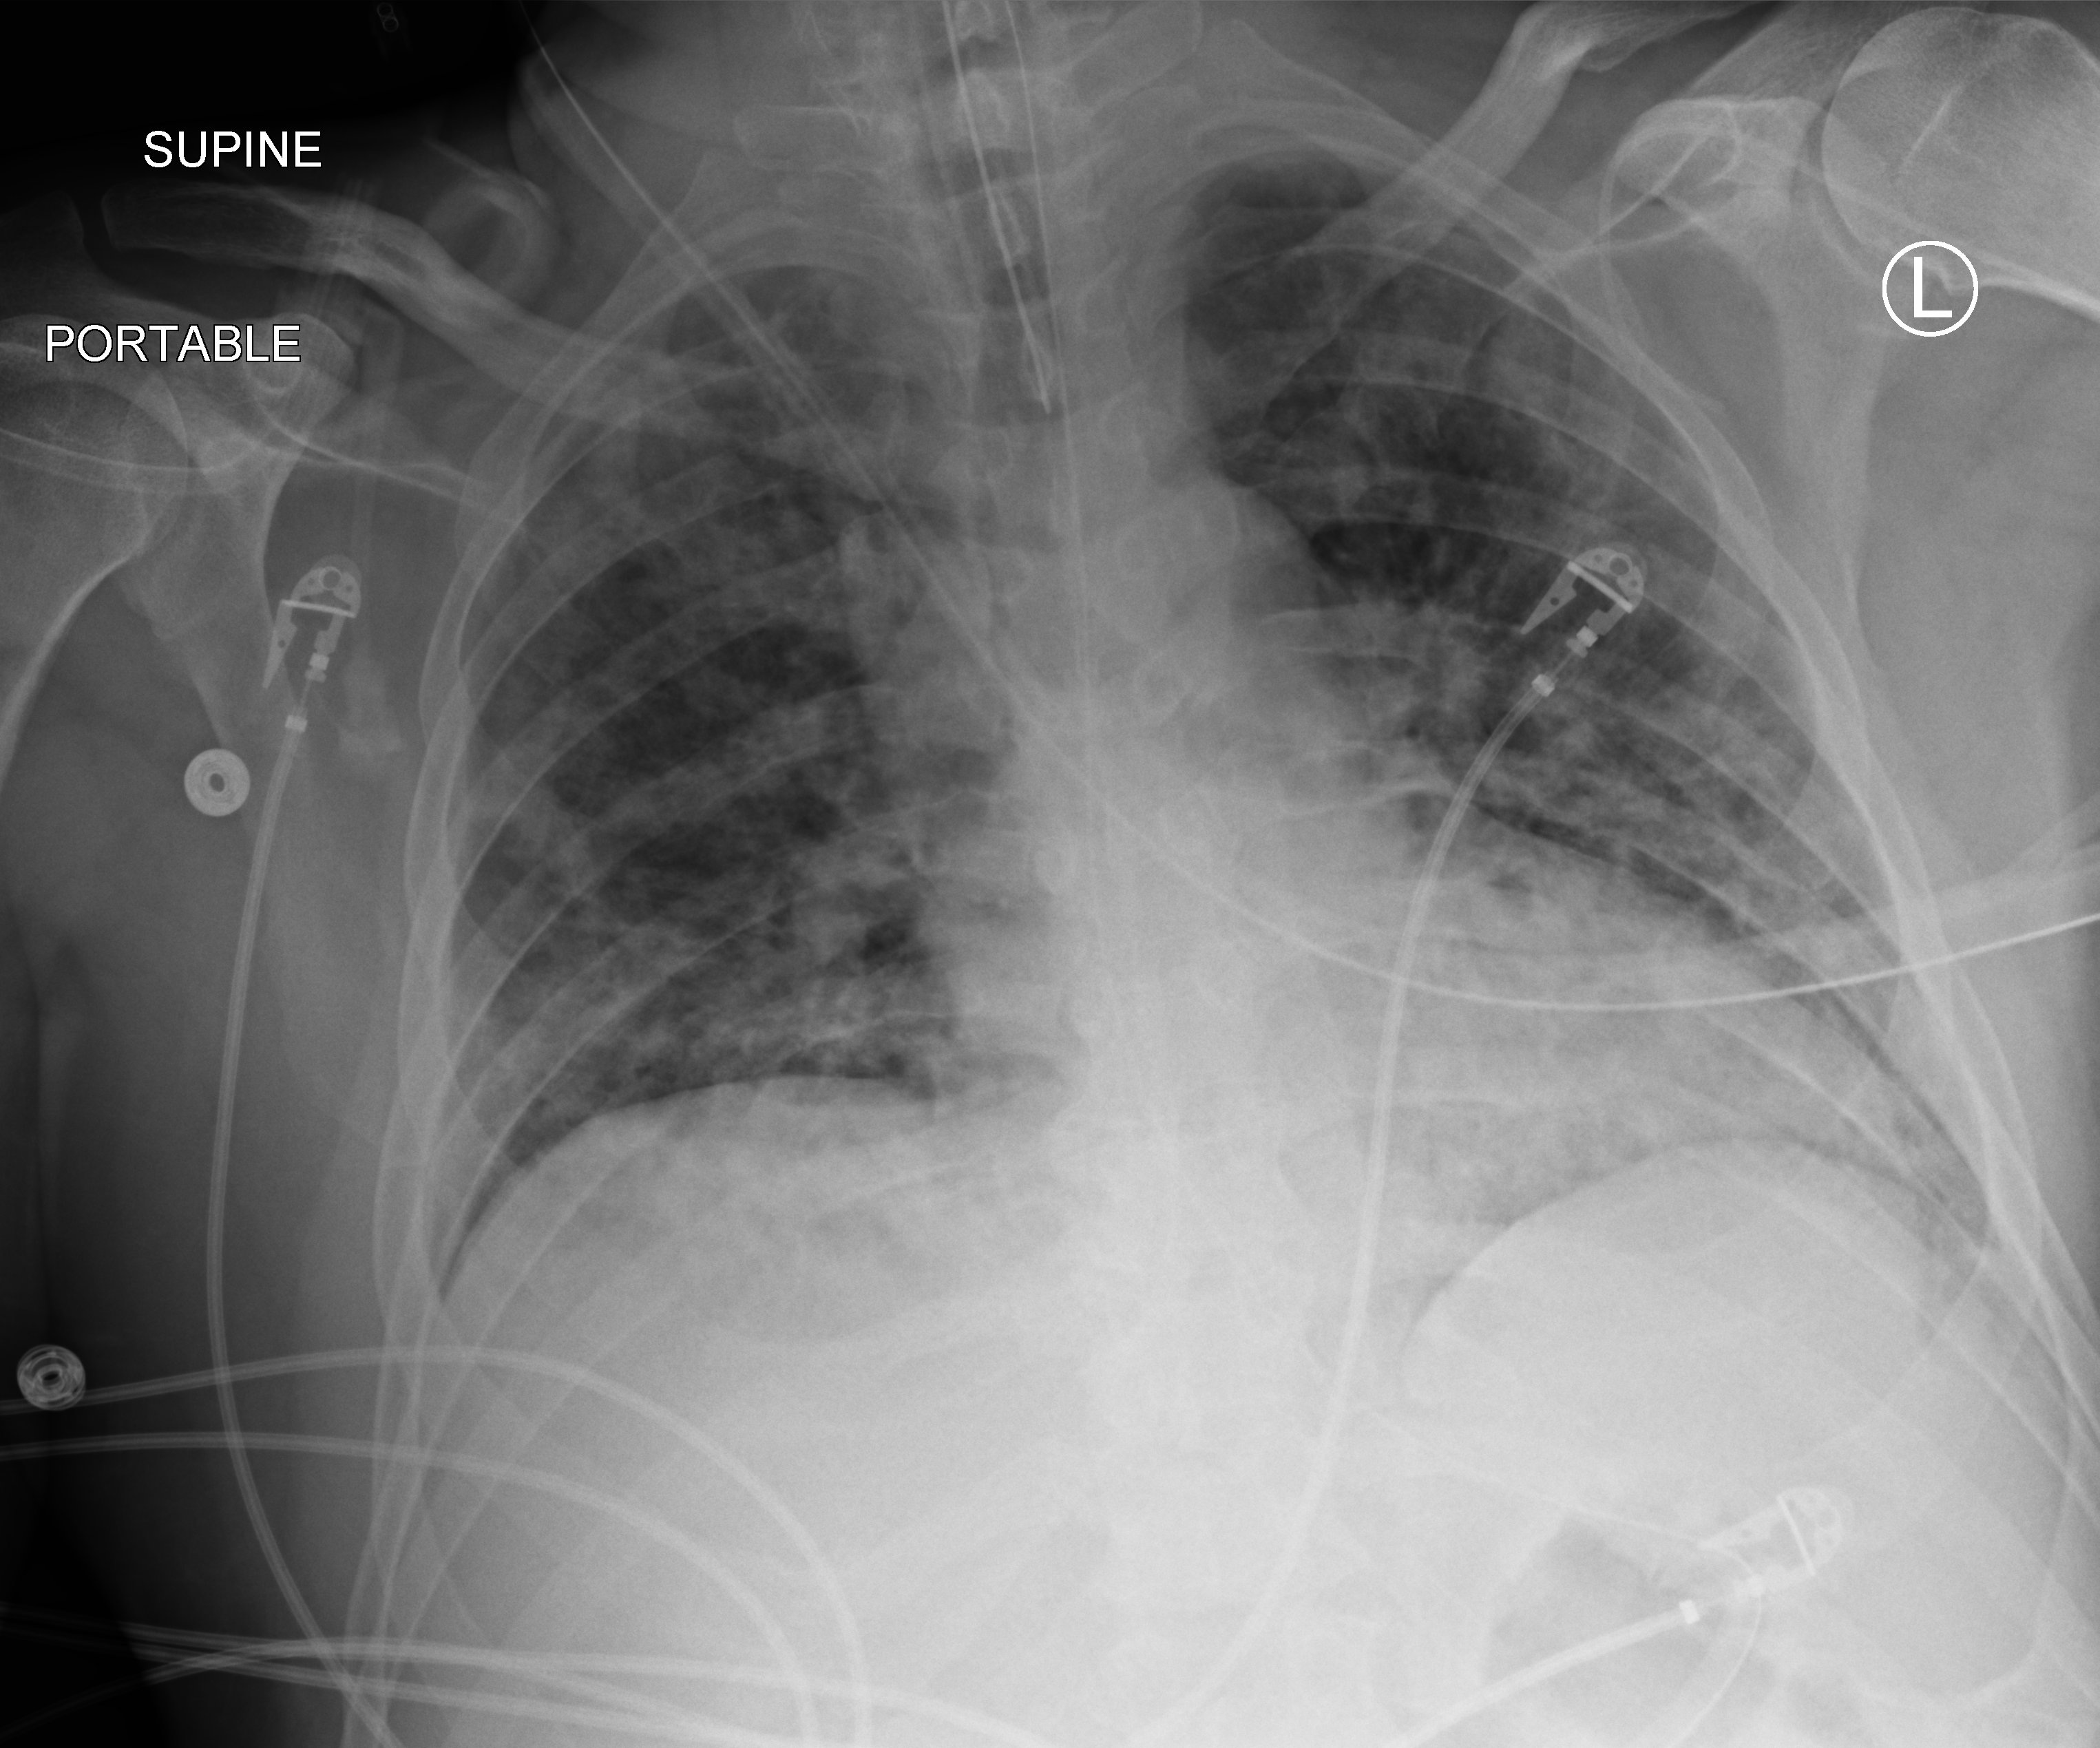
Portable chest radiograph, anteroposterior (AP) projection. Male patient hospitalised with COVID-19, age 18–59 years.
Admission-level facts for this patient (not findings on this image; timing relative to this image not recorded): mechanically ventilated during this hospital stay: yes.